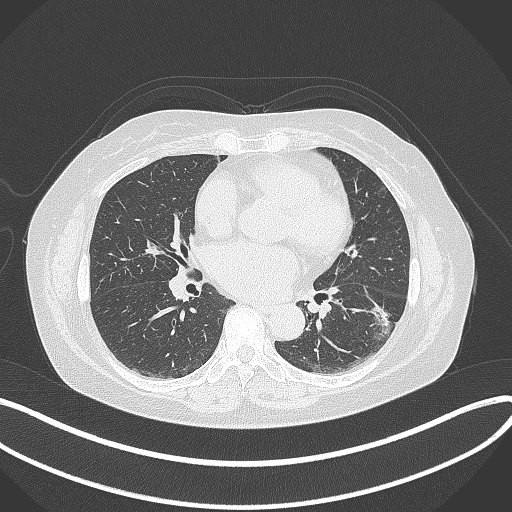
Chest CT, one axial slice; position 170 of 373 along the scan axis; 120 kVp; lung window (W 1500 / L -600 HU); 1 mm slice thickness; 512 × 512 image matrix. Female patient, age 67 years. Case-level facts recorded for this patient, not image findings: clinical TNM (as recorded): T1c N0 M0; histopathological grade: G2.
Annotated regions visible in this slice (rectangle marked by the reading radiologist):
- lung tumour (recorded histology: adenocarcinoma): bounding box <363,300,398,333> (left, top, right, bottom; pixels)